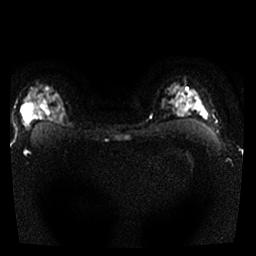
Breast MRI, one axial slice; position 22 of 25 along the scan axis; diffusion-weighted series; image 2 of 4 stored at this slice position (different b-values; order by instance number); 1.5 T; 4 mm slice thickness; 256 × 256 image matrix, field of view 300 × 300 mm. Female patient.
Annotated regions visible in this slice (manually delineated by an expert):
- tumour on diffusion-weighted imaging: bounding box (x1, y1, x2, y2) in pixels: (22, 97, 56, 117)